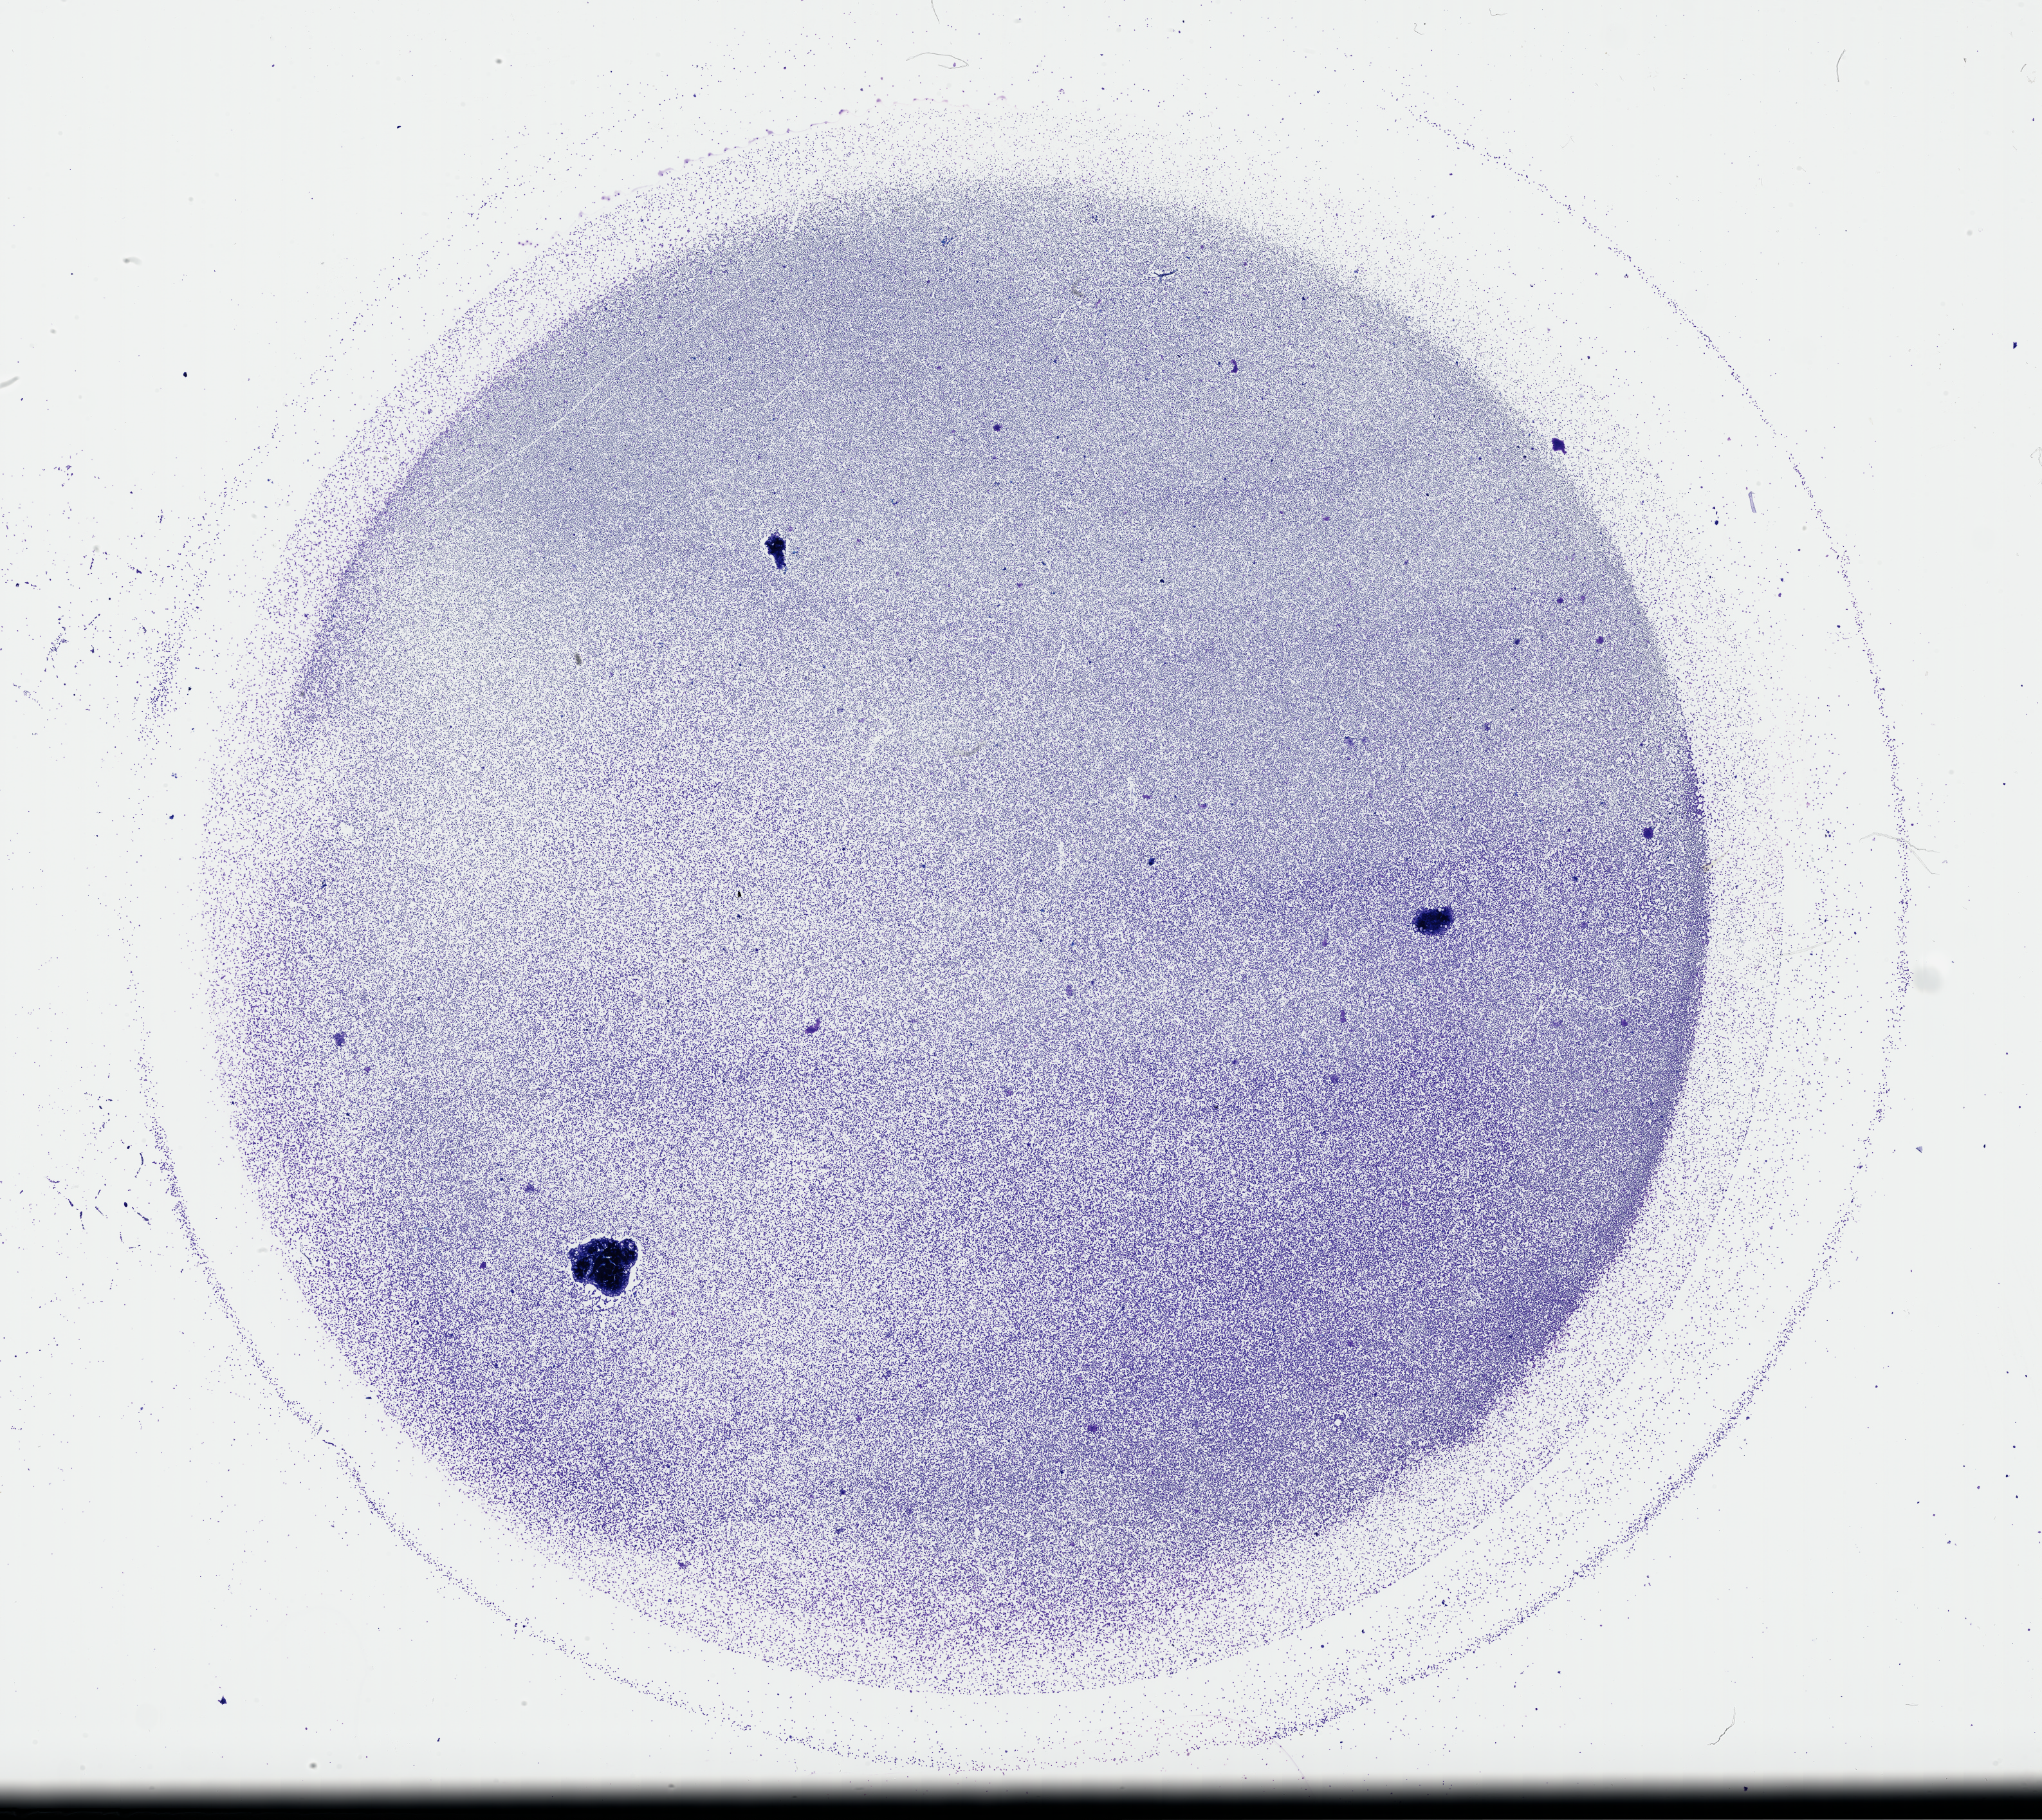
Whole-slide histology image, H&E-stained, a low-resolution overview of the entire scanned area, about 25.6 x 22.8 mm. Bone marrow (leukaemic) sample. Male, 63 y/o. Blasts: 80%.
- WHO classification: AML with maturation
- FAB classification: M2
- diagnosis: Acute Myeloid Leukemia